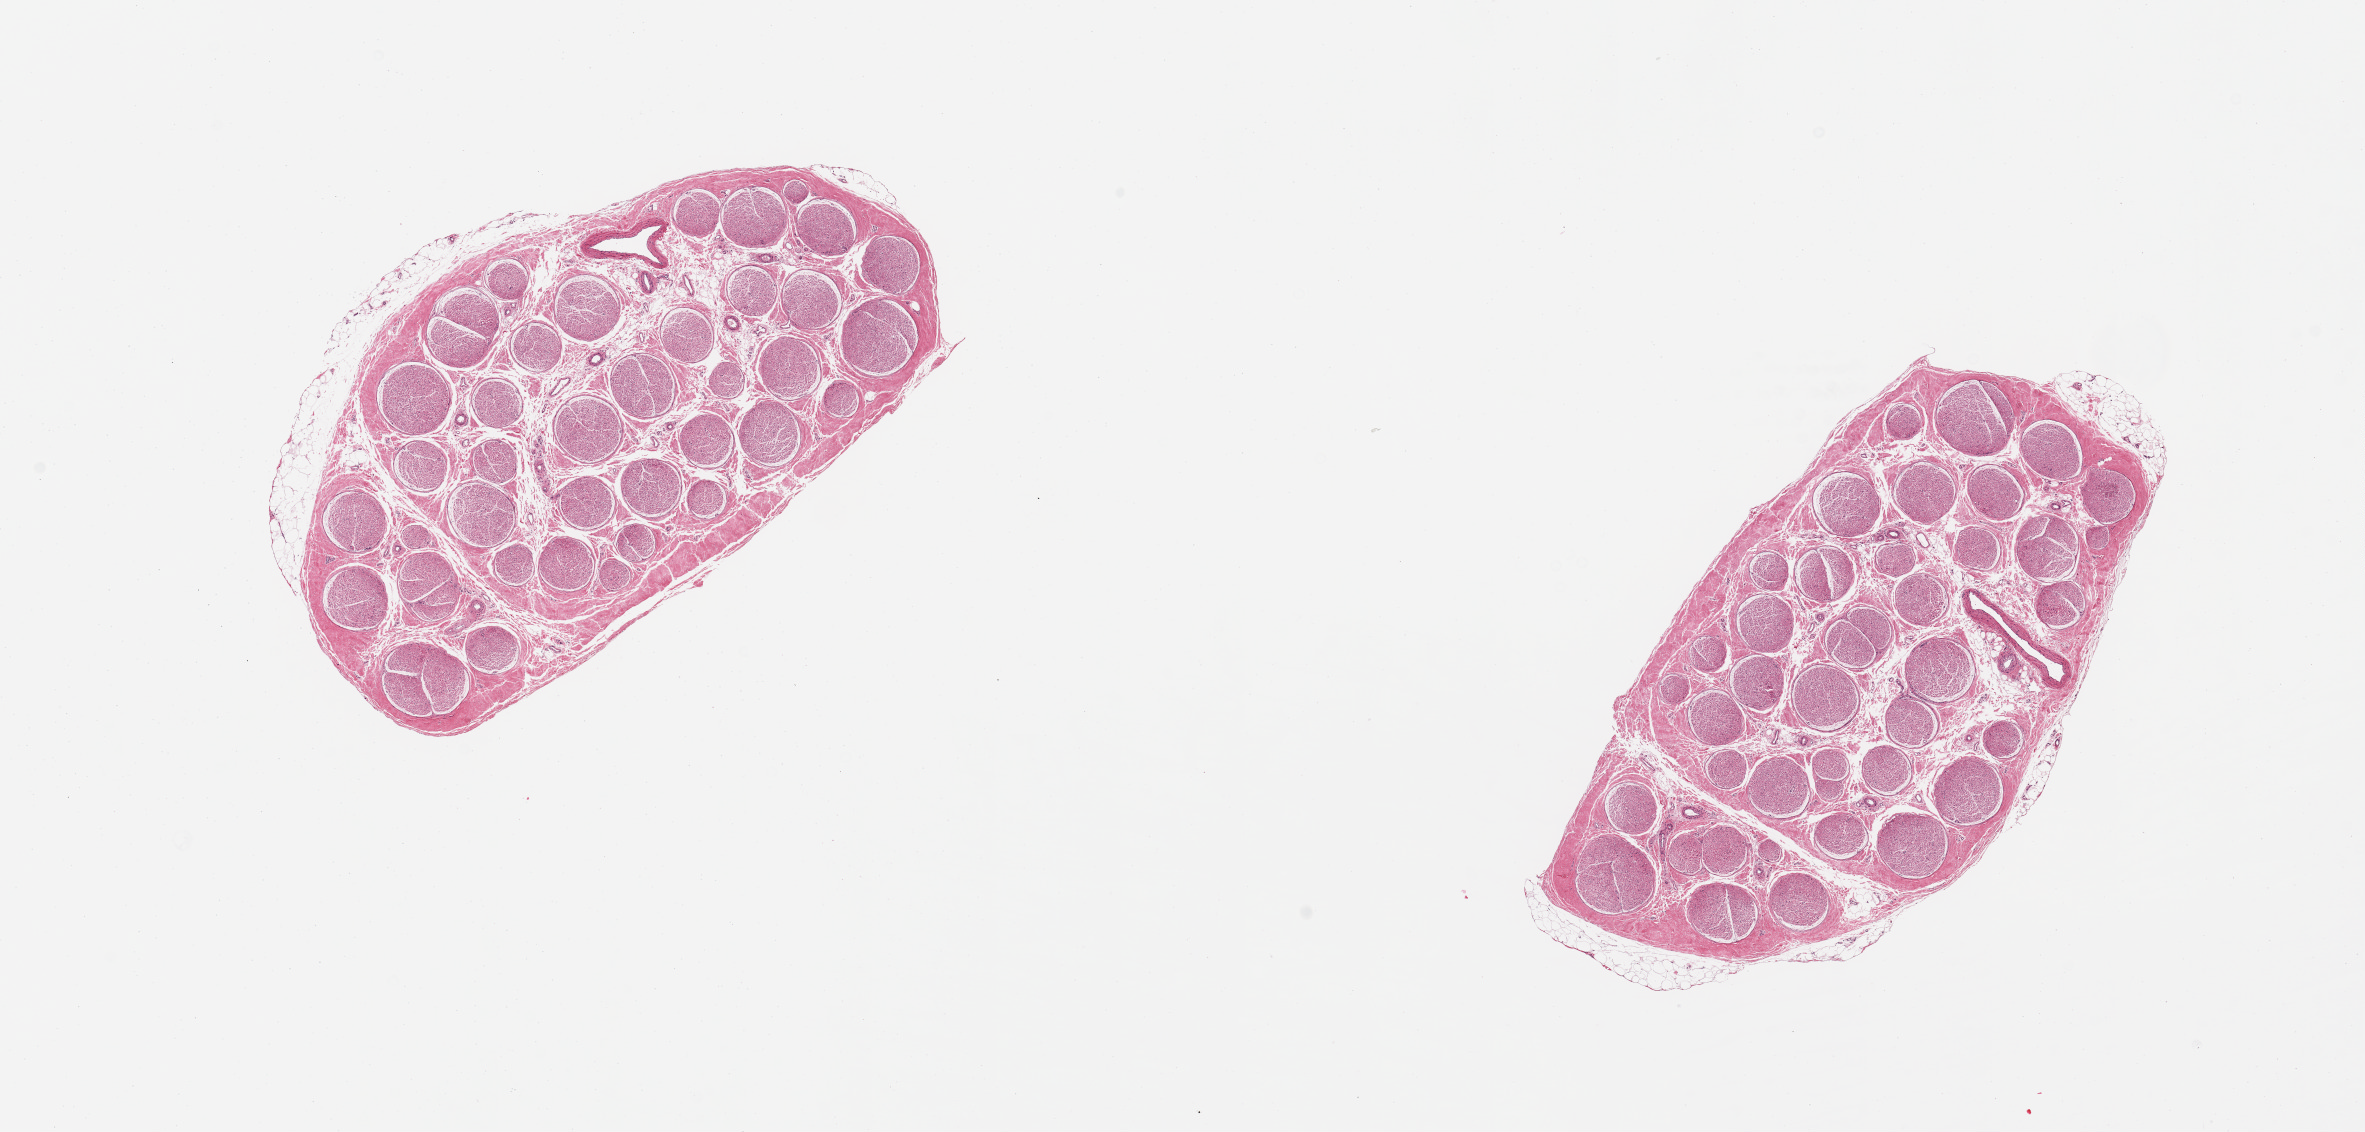
Hematoxylin and eosin (H&E) whole-slide image, brightfield, whole scanned area (about 18.7 x 9.0 mm) shown as a low-resolution overview; PAXgene-fixed paraffin-embedded (PFPE) section; section of tibial nerve (target tissue); tissue donor sample. Donor: male.
Reviewer comment on this tissue sample: 2 pieces; well trimmed with minimal attached fat.